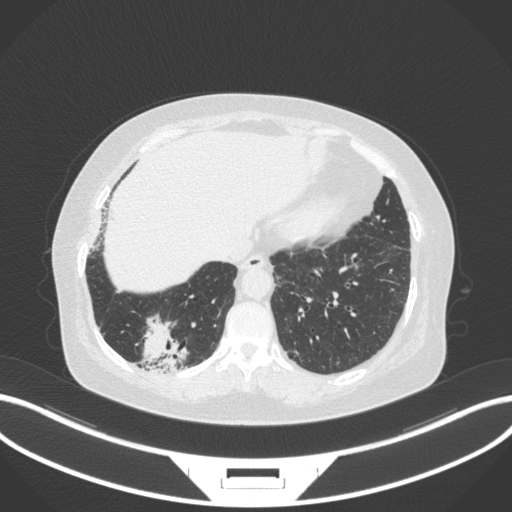
Chest CT, one axial slice; slice 38 of 303 in the series (ordered by position); reconstruction kernel B31f; lung window (W 1500 / L -600 HU); 1 mm slice thickness; 512 × 512 image matrix, field of view 400 × 400 mm. Female patient, age 65 years. From the clinical record (not read from this slice): clinical TNM (as recorded): T2b N1 M0.
Outlined on this slice (rectangle marked by the reading radiologist):
- lung tumour (recorded histology: adenocarcinoma): box from (x=135, y=310) to (x=192, y=372) px